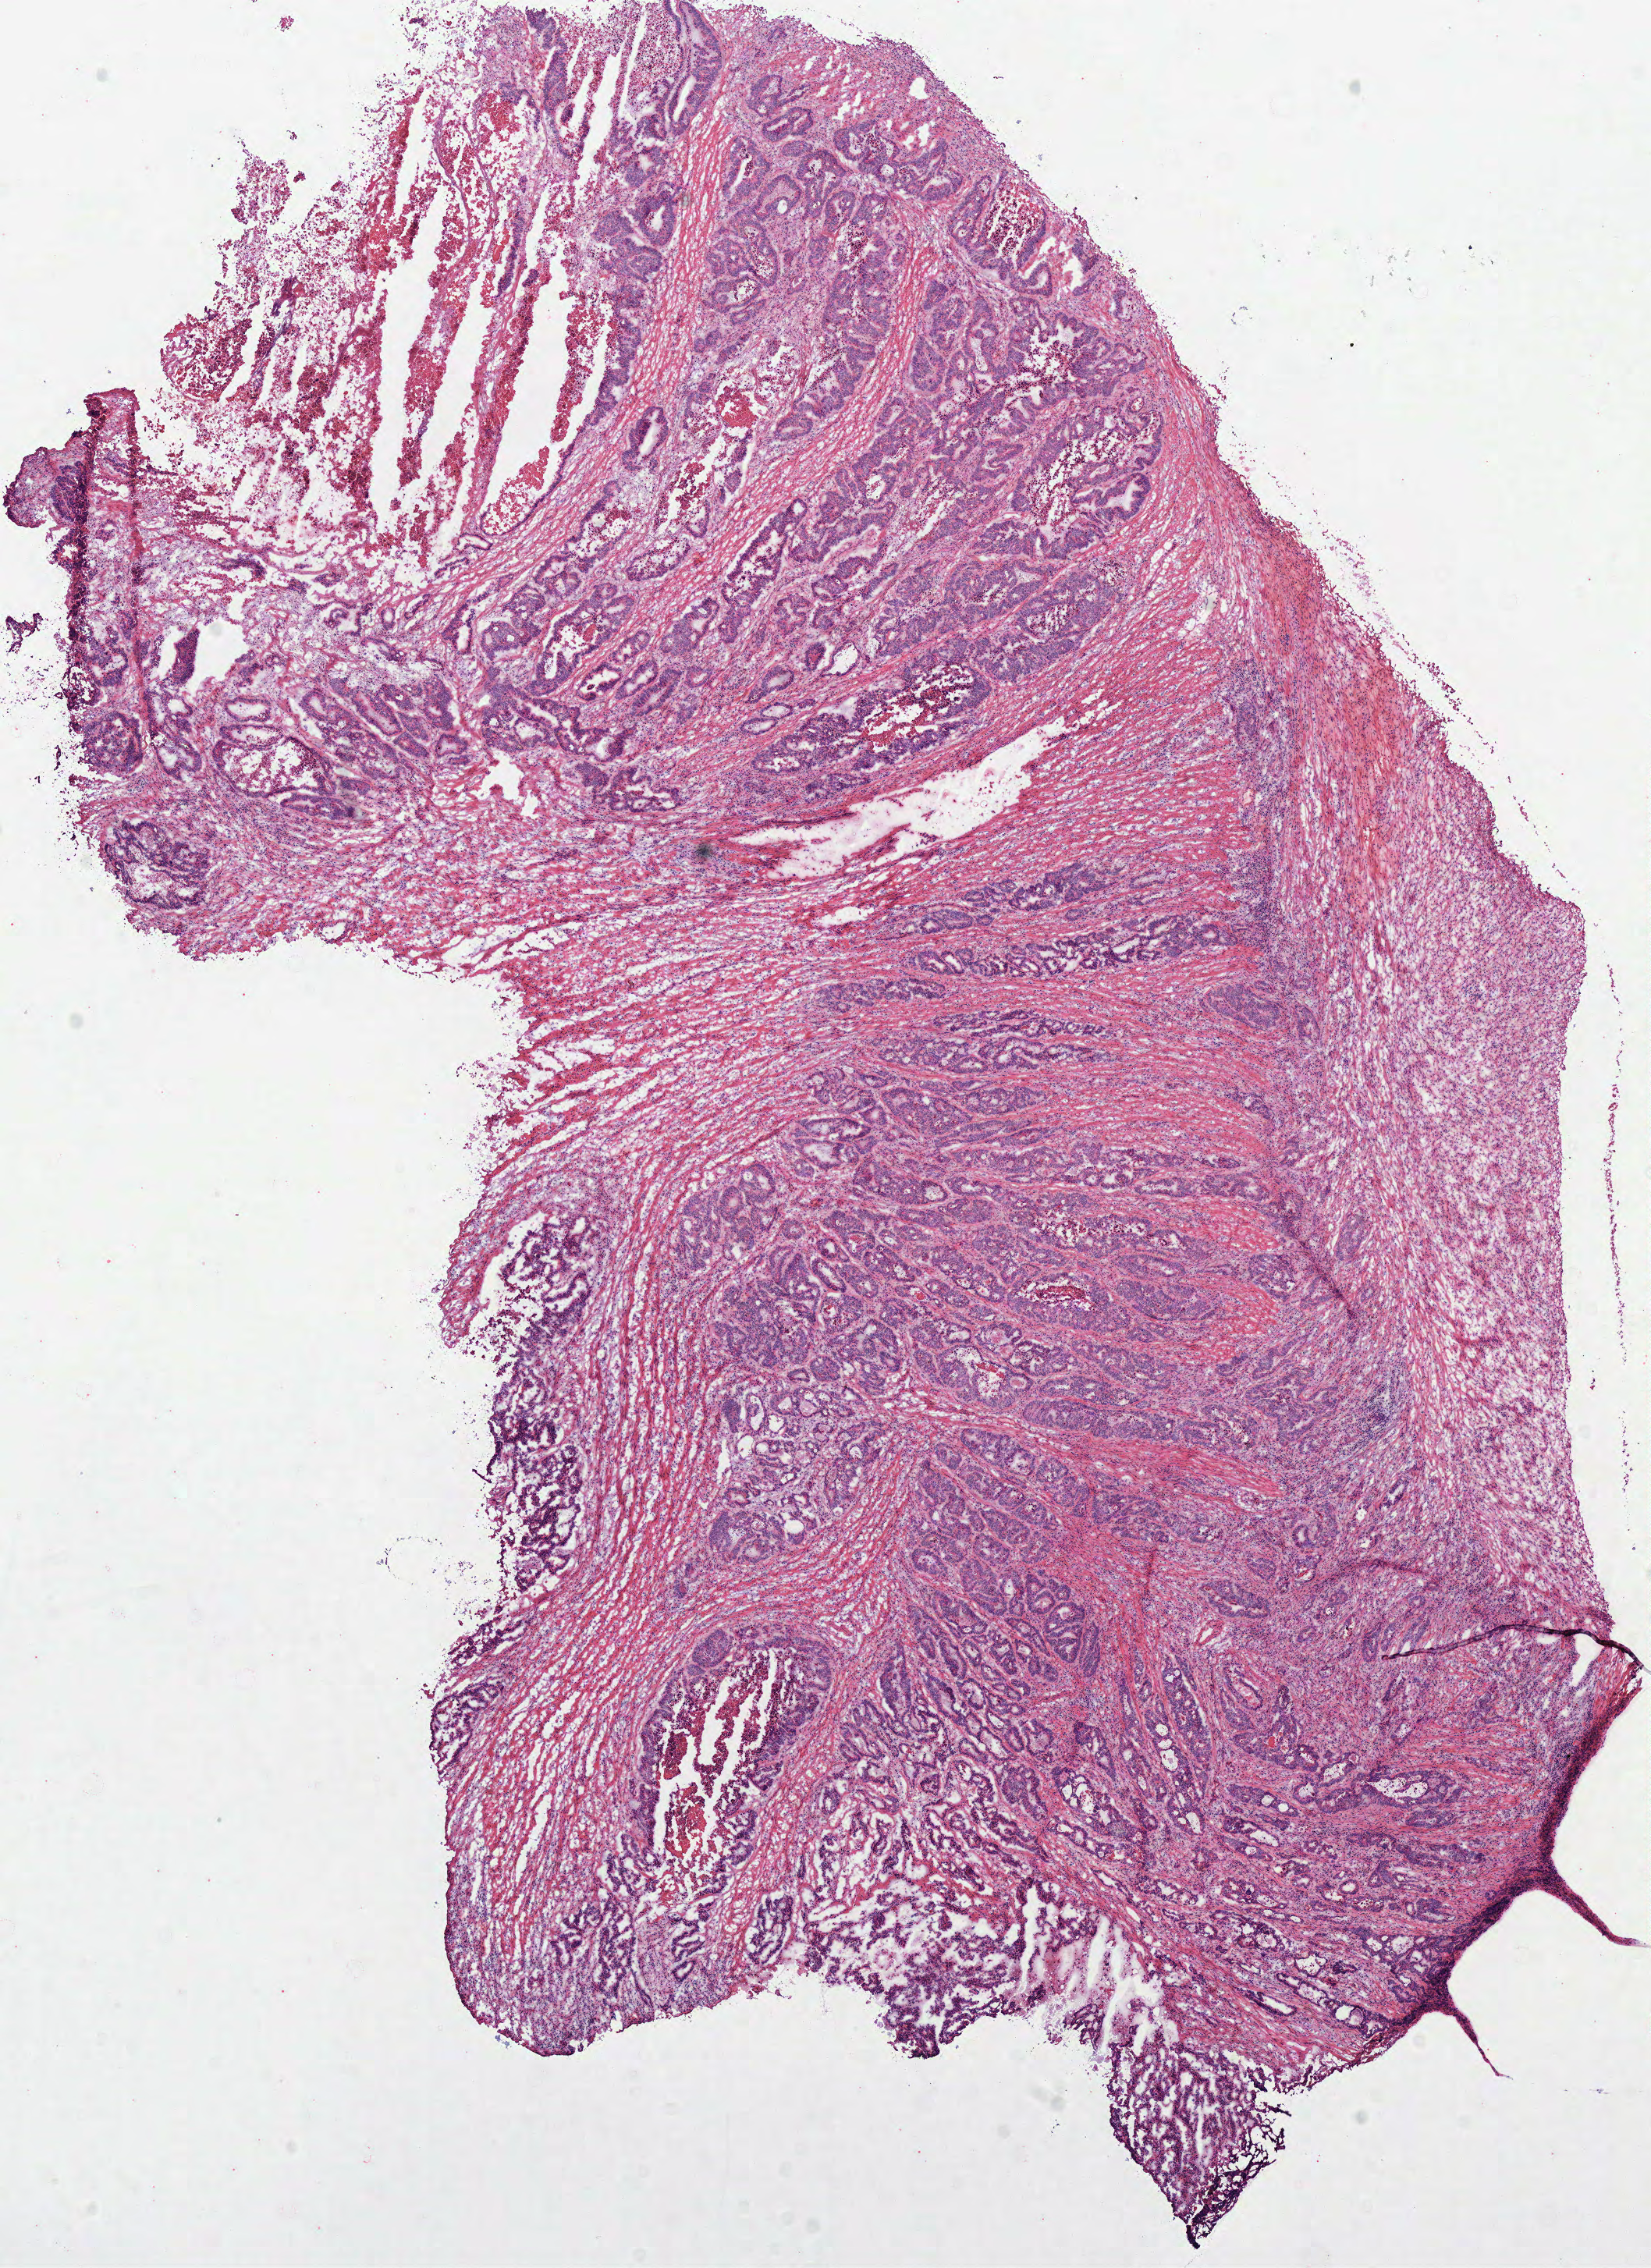
H&E-stained whole-slide image — whole scanned area (about 8.3 x 11.4 mm, acquisition: 40x scan) shown as a low-resolution overview. Frozen section from the top of the tissue portion. Primary tumour sample from the colon. Patient: male, age at initial diagnosis 77 years. Slide review estimates, as recorded: tumour cells 60%, tumour nuclei 75%, normal cells 0%, stromal cells 30%, necrosis 15%.
* pathologic diagnosis: Adenocarcinoma, NOS (descending colon)
* AJCC pathologic stage: IIA (6th edition)